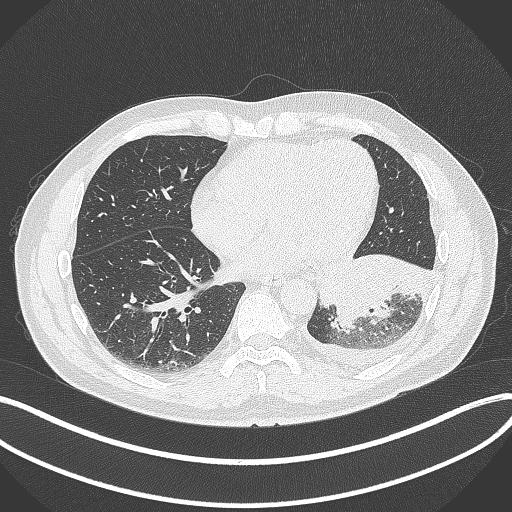
Chest CT, one axial slice; slice 127 of 342 in the series (ordered by position); reconstruction kernel B70f; lung window (W 1500 / L -600 HU); 1 mm slice thickness; 512 × 512 image matrix, field of view 400 × 400 mm. Male patient, age 58 years. Case-level facts recorded for this patient, not image findings: clinical TNM (as recorded): T3 N1 M1b; histopathological grade: G3.
Annotated regions visible in this slice (bounding box drawn by a radiologist):
- lung tumour (recorded histology: small cell carcinoma): bounding box <315,246,431,335> (left, top, right, bottom; pixels)